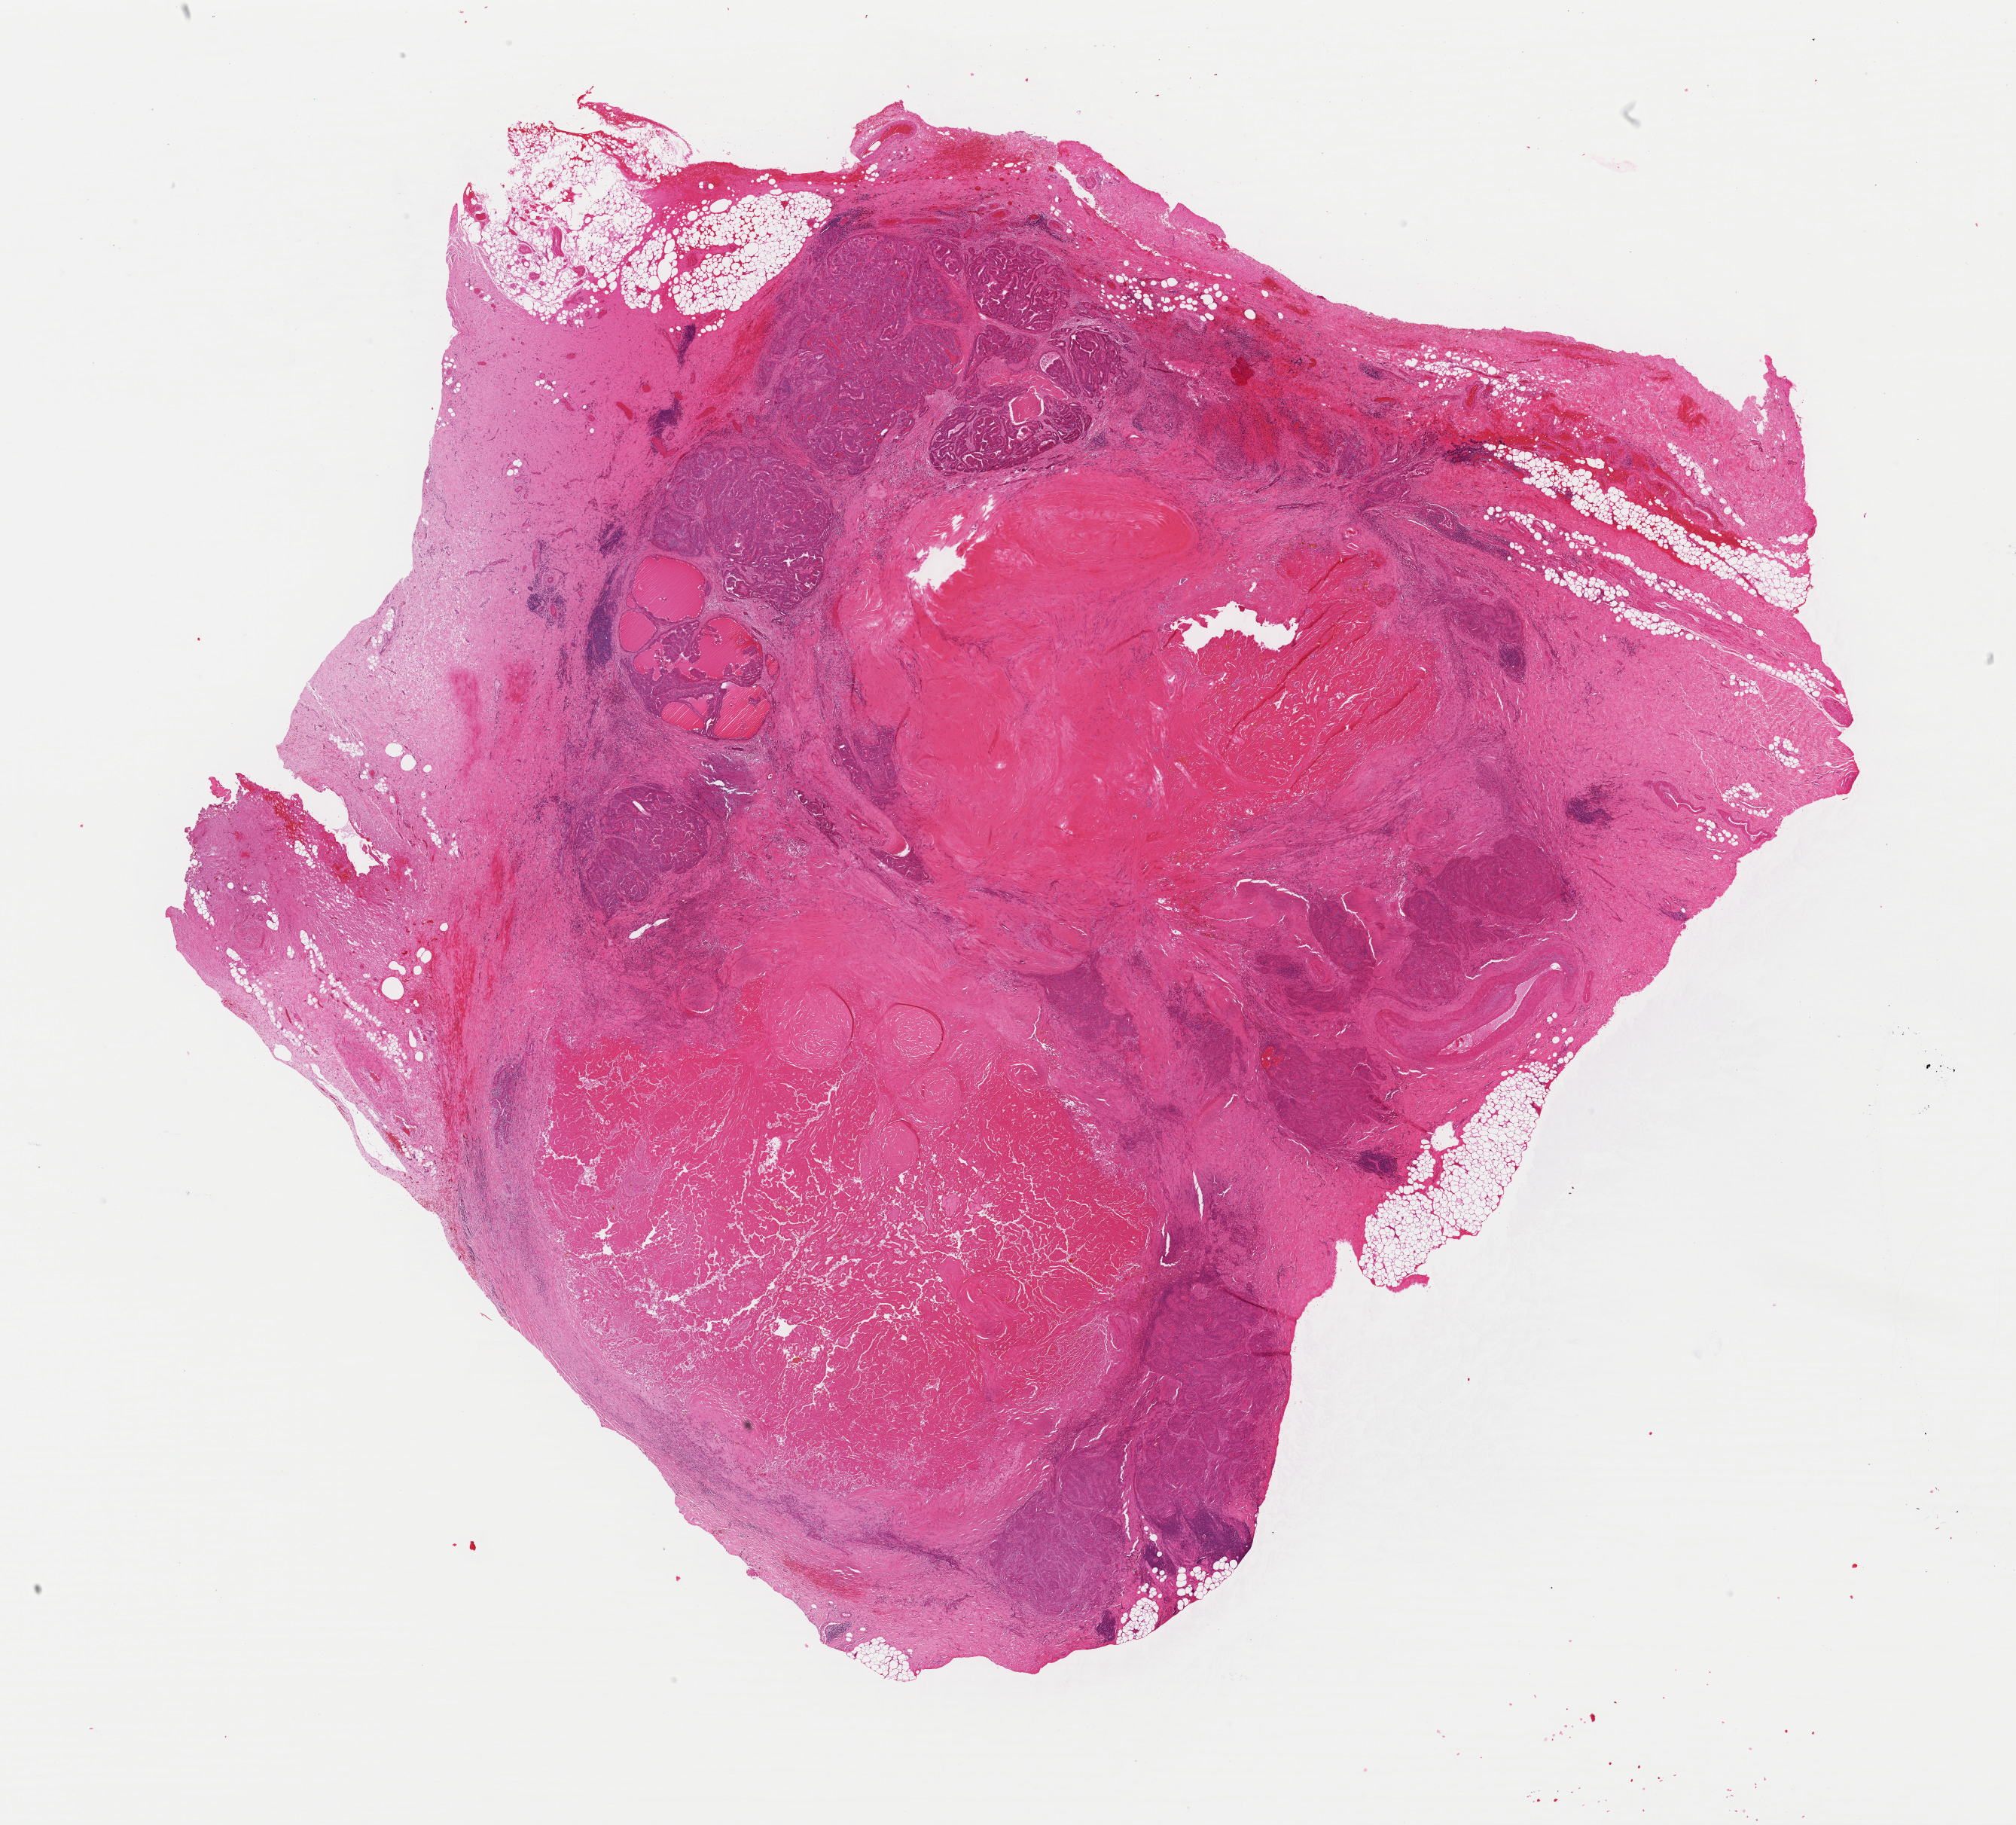
Hematoxylin and eosin (H&E) stained whole-slide image, whole scanned area (about 21.1 x 19.1 mm, from a 40x scan) shown as a low-resolution overview, formalin-fixed paraffin-embedded (FFPE) diagnostic section, sample: primary tumour, thyroid. Male patient; age at initial diagnosis 83 years.
Diagnosis: Papillary adenocarcinoma, NOS (thyroid gland).